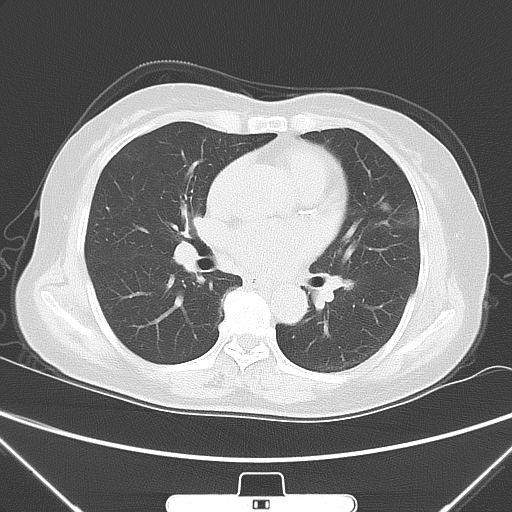
Chest CT, one axial slice. Position 29 of 60 along the scan axis. 120 kVp. Lung window (W 1500 / L -600 HU). 5 mm slice thickness. 512 × 512 image matrix. Female patient, age 70 years. Case-level facts recorded for this patient, not image findings: clinical TNM (as recorded): T1b N0 M0; histopathological grade: G2.
Outlined on this slice (rectangle marked by the reading radiologist):
- lung tumour (recorded histology: adenocarcinoma): bounding box (x1, y1, x2, y2) in pixels: (371, 188, 398, 221)